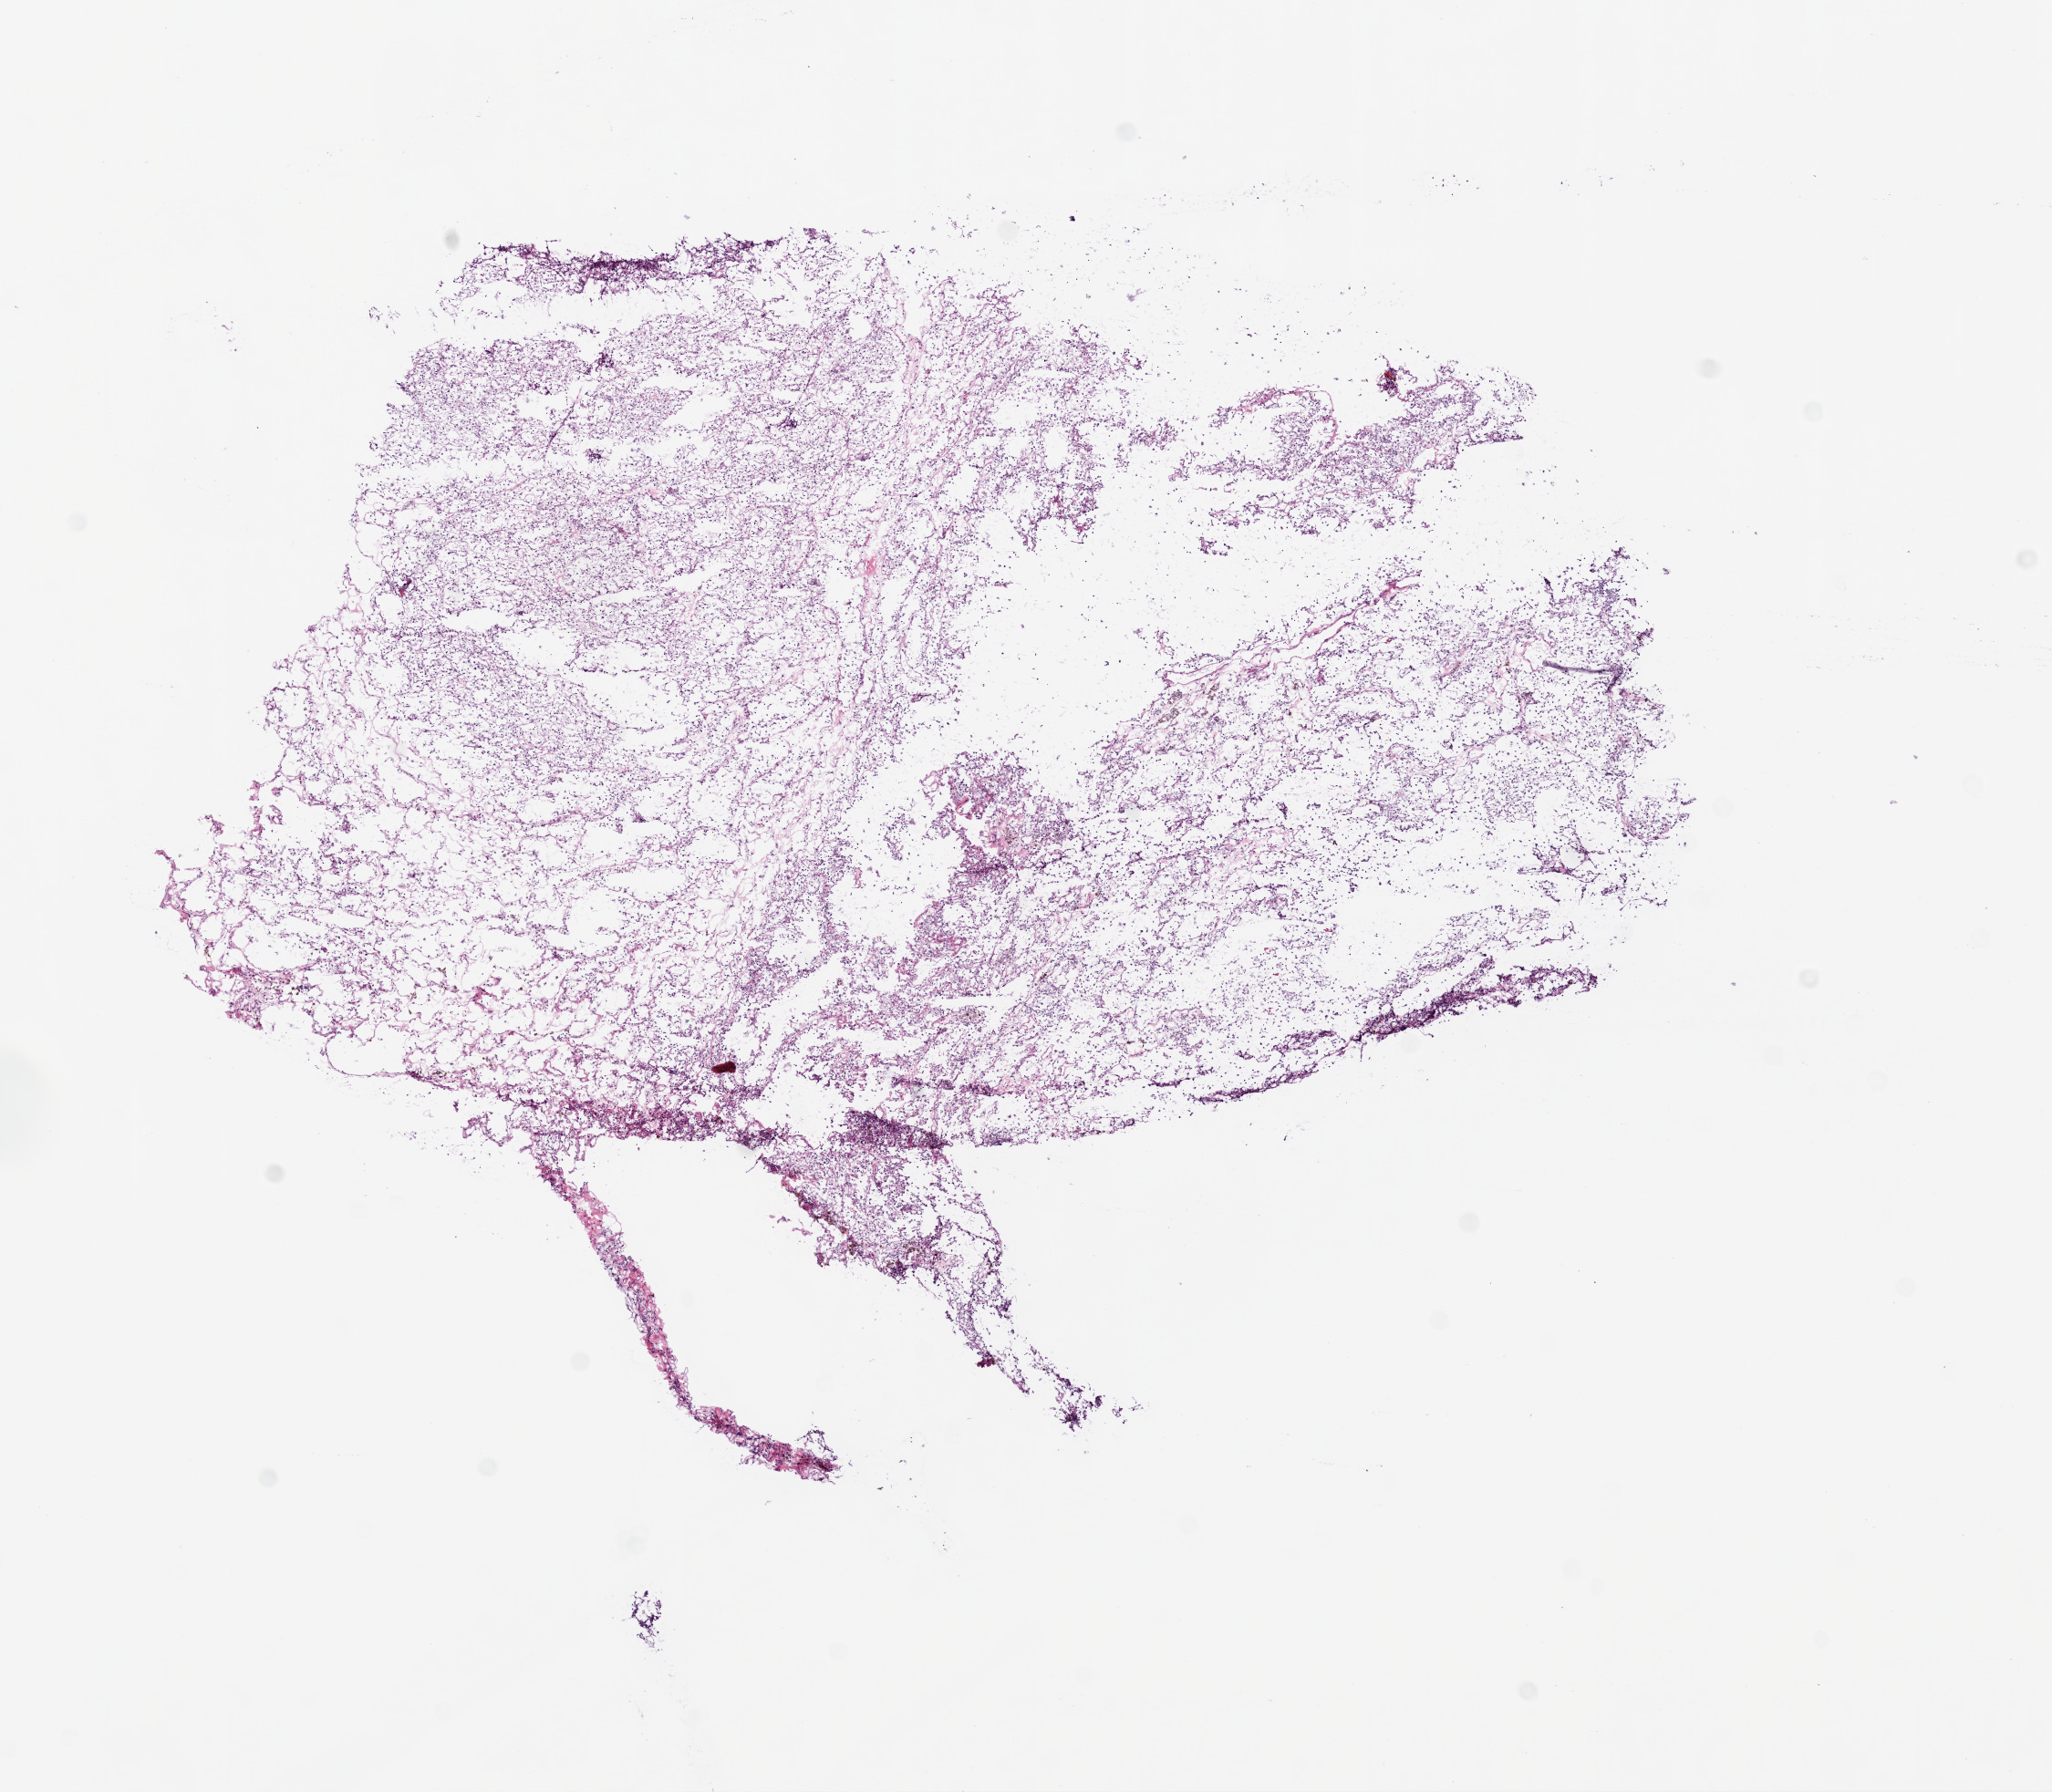
H&E-stained whole-slide image — a low-resolution overview of the entire scanned area, about 9.0 x 7.9 mm (slide scanned at 20x); frozen section; kidney, primary tumour sample. Female, age 57 years at initial diagnosis. Histologic grade: G2 (moderately differentiated). Composition of this section per pathologist review: tumour cells 95%, tumour nuclei 60%, normal cells 0%, stromal cells 5%, necrosis 0%.
• AJCC pathologic stage: I
• laterality: left
• pathologic diagnosis: Clear cell adenocarcinoma, NOS